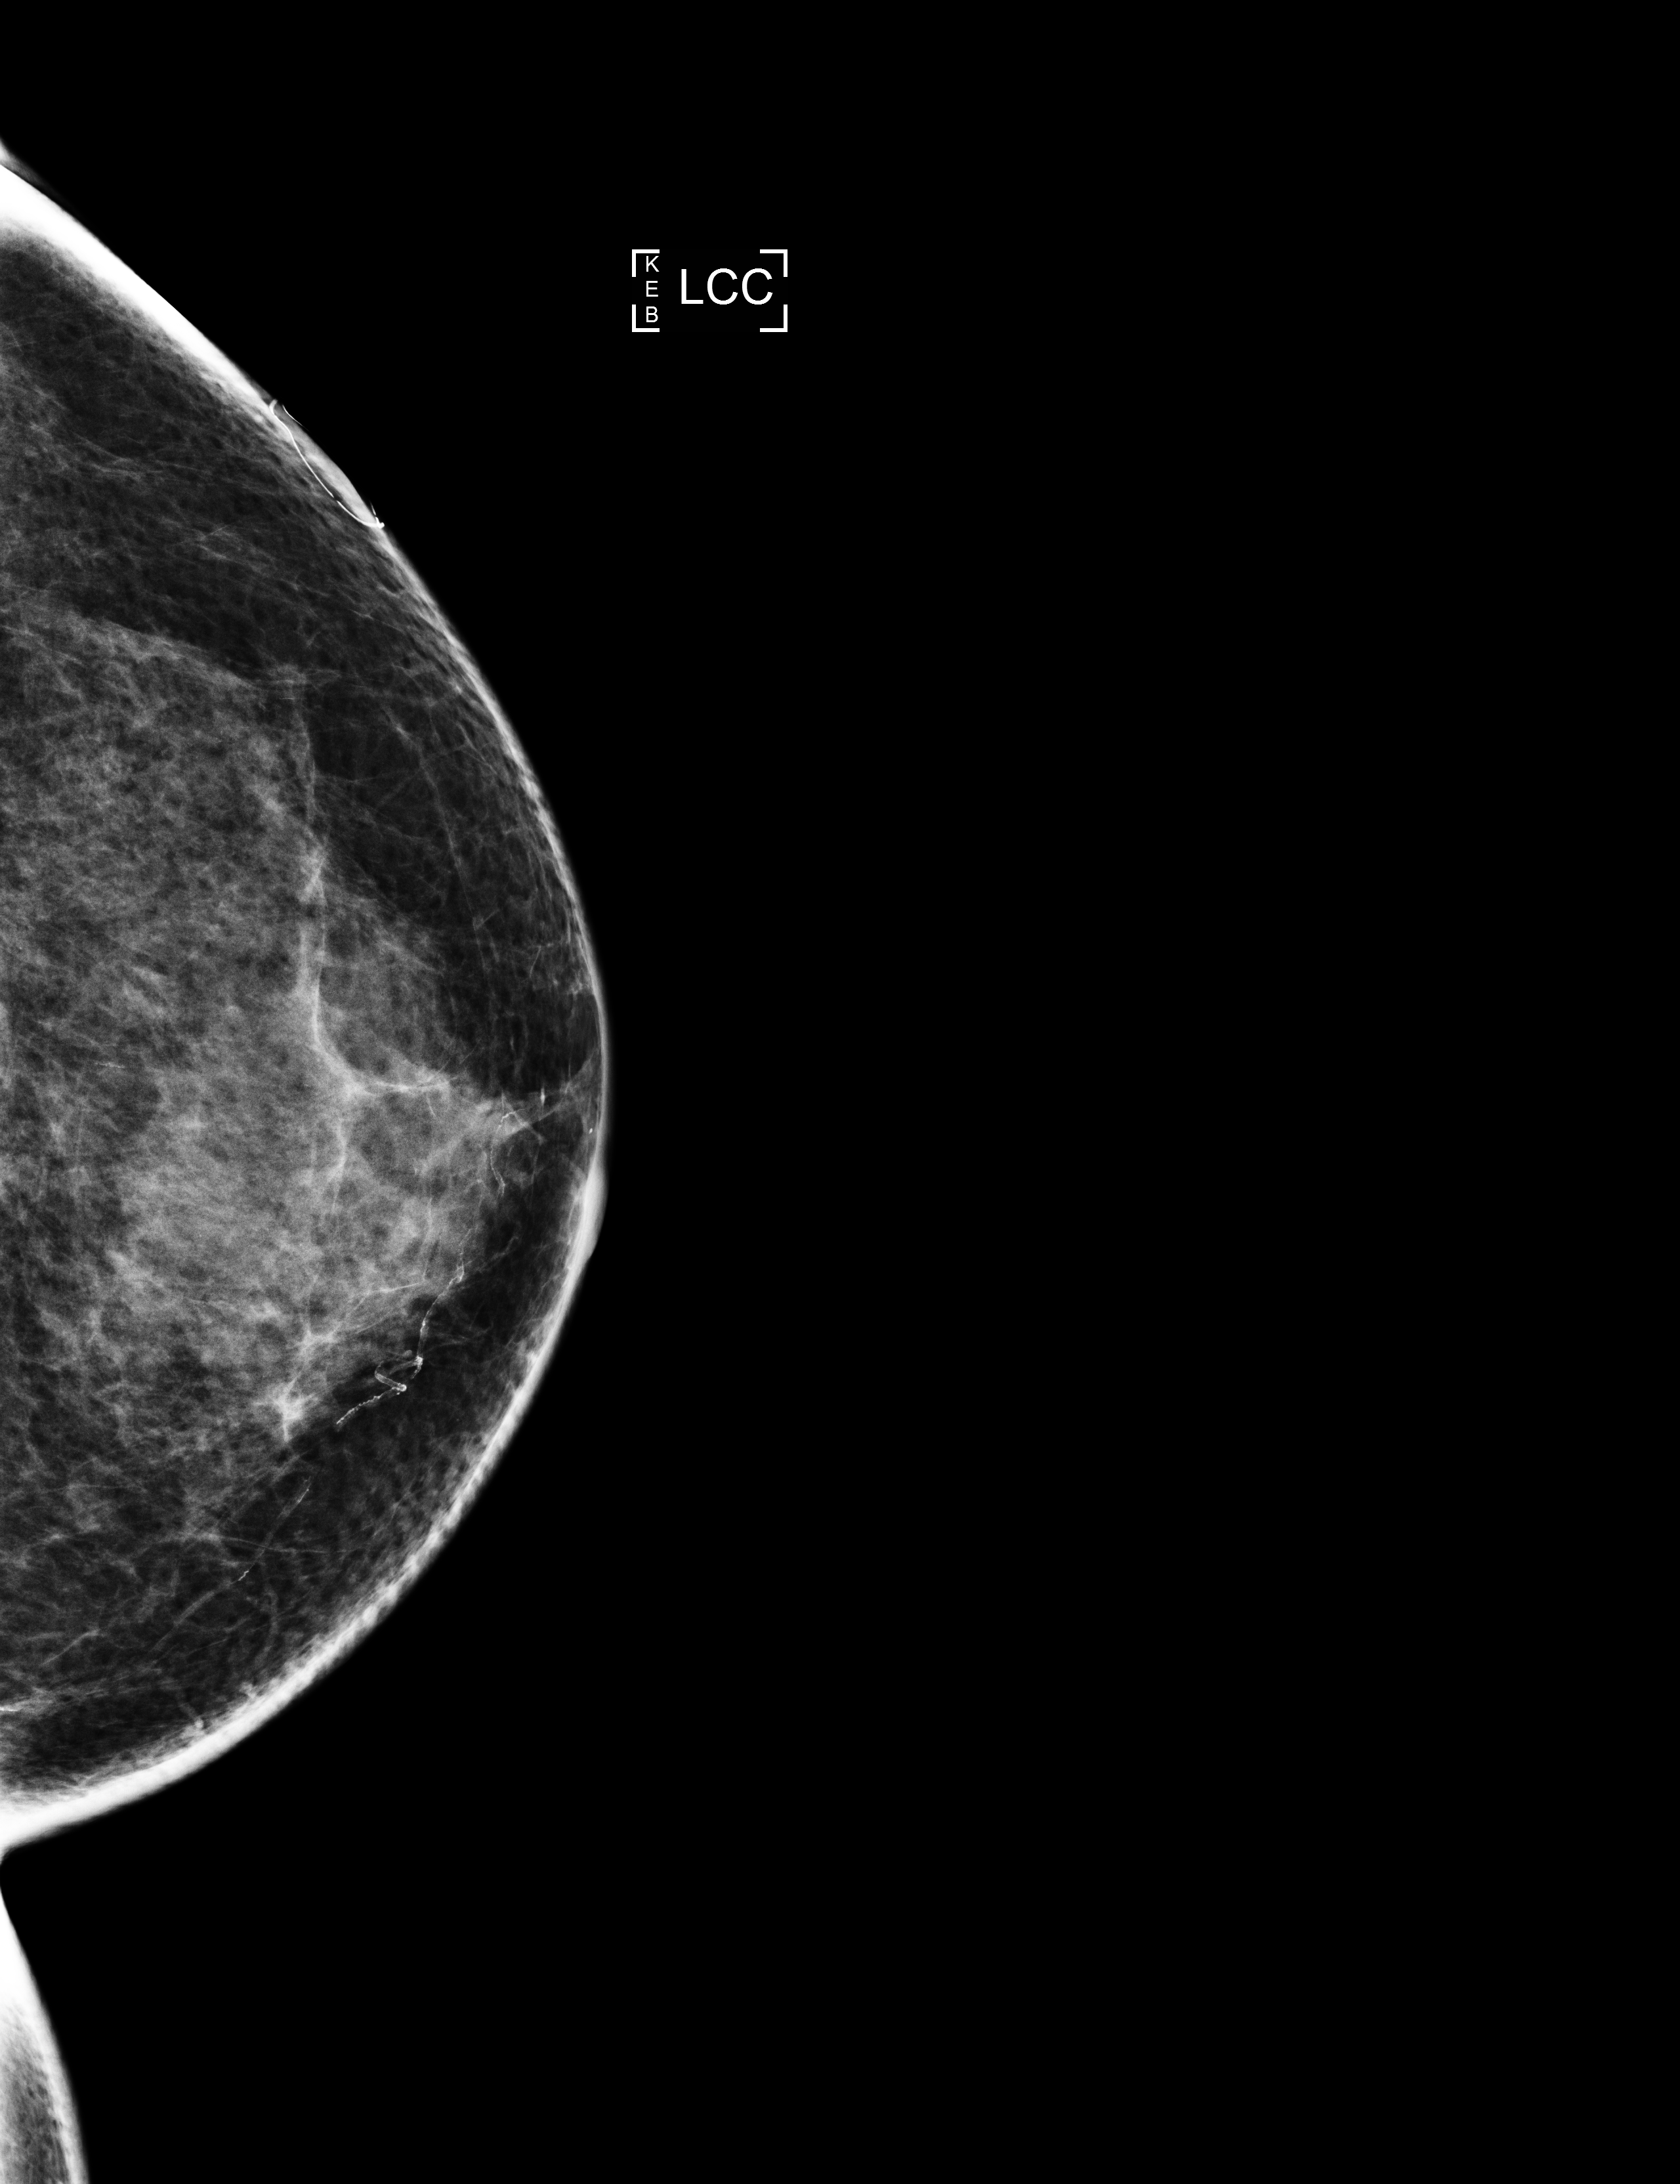
Screening examination, compressed breast thickness 49 mm, system: Selenia Dimensions. Patient: female, 65 years.
Image type: full-field digital mammogram. Breast: left. Projection: cranio-caudal projection.